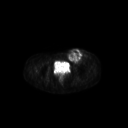
FDG PET of an extremity soft-tissue mass (from a PET/CT study), one axial slice. Position 69 of 267 along the scan axis. 3.27 mm slice thickness. 128 × 128 image matrix, field of view 600 × 600 mm. Female patient, age 24 years. Case-level facts recorded for this patient, not image findings: histological type: leiomyosarcoma; grade: high; site of the primary tumour: groin.
Structures marked on this image (expert contour drawn on MRI and transferred to this co-registered scan by the dataset authors):
- gross tumour volume including surrounding oedema: bounding box <66,48,90,65> (left, top, right, bottom; pixels)
- gross tumour volume (mass): <66,49,83,64>